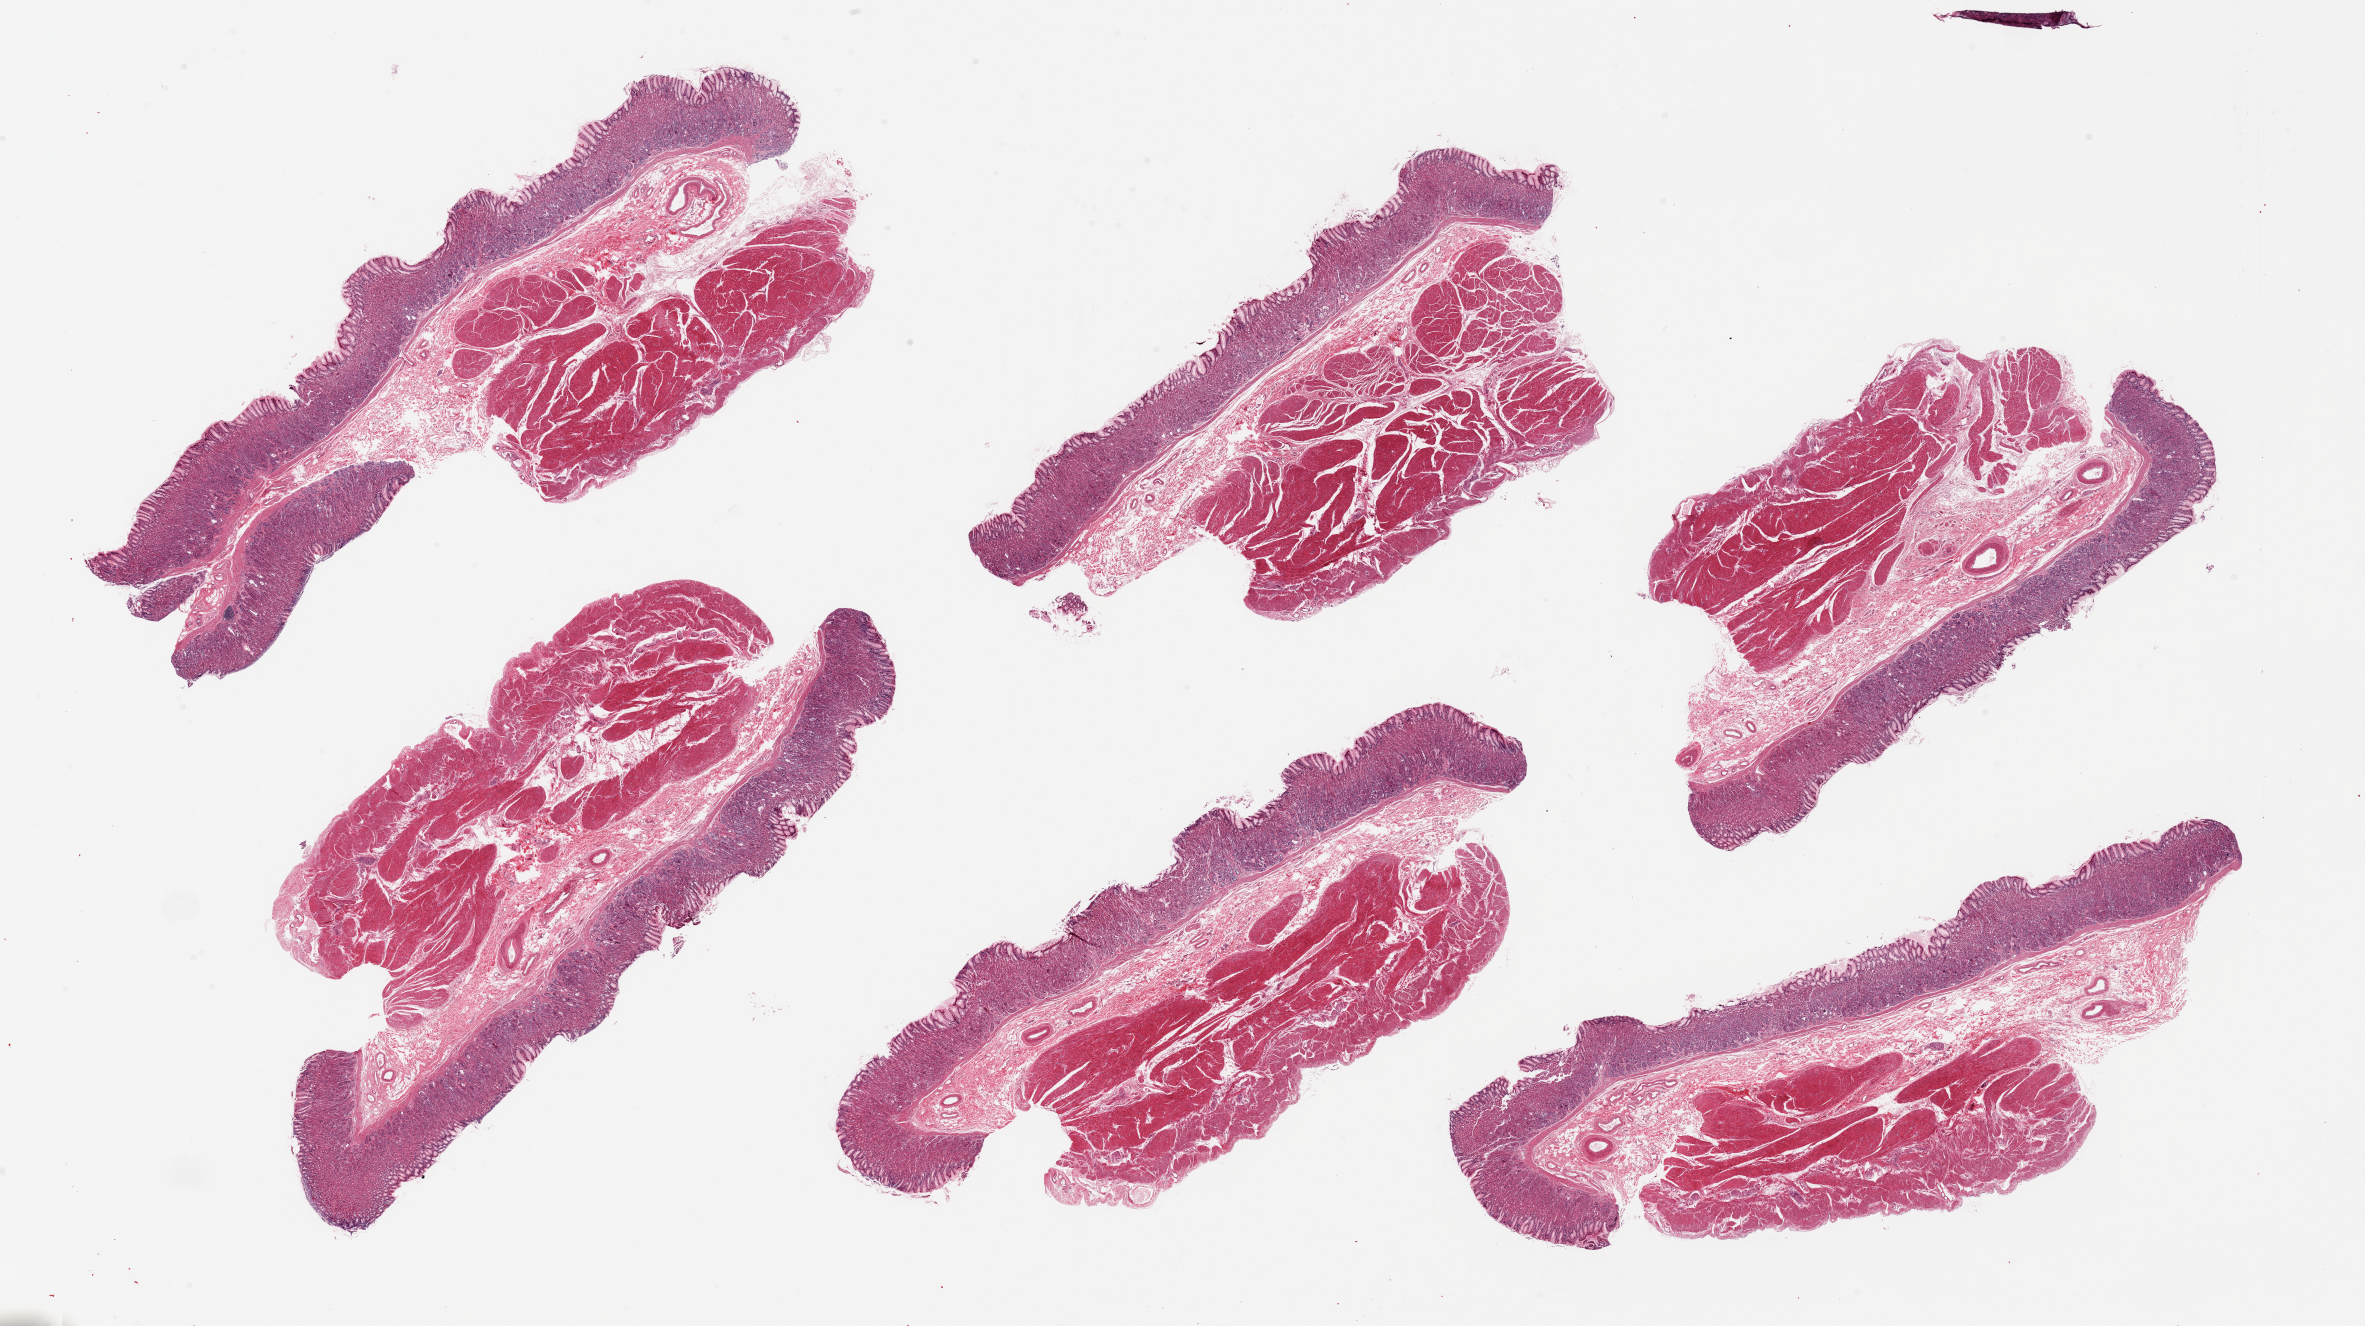
Whole-slide image, hematoxylin and eosin (H&E) stain, brightfield — shown as a low-resolution overview of the whole scanned area (about 37.4 x 21.0 mm), PAXgene-fixed paraffin-embedded (PFPE) section, sampled site (target tissue): stomach, donor tissue sample. Donor sex: female.
- review note (as recorded): 6 pieces, mucosa well-preserved, up to 1mm, ~20-30% thickness